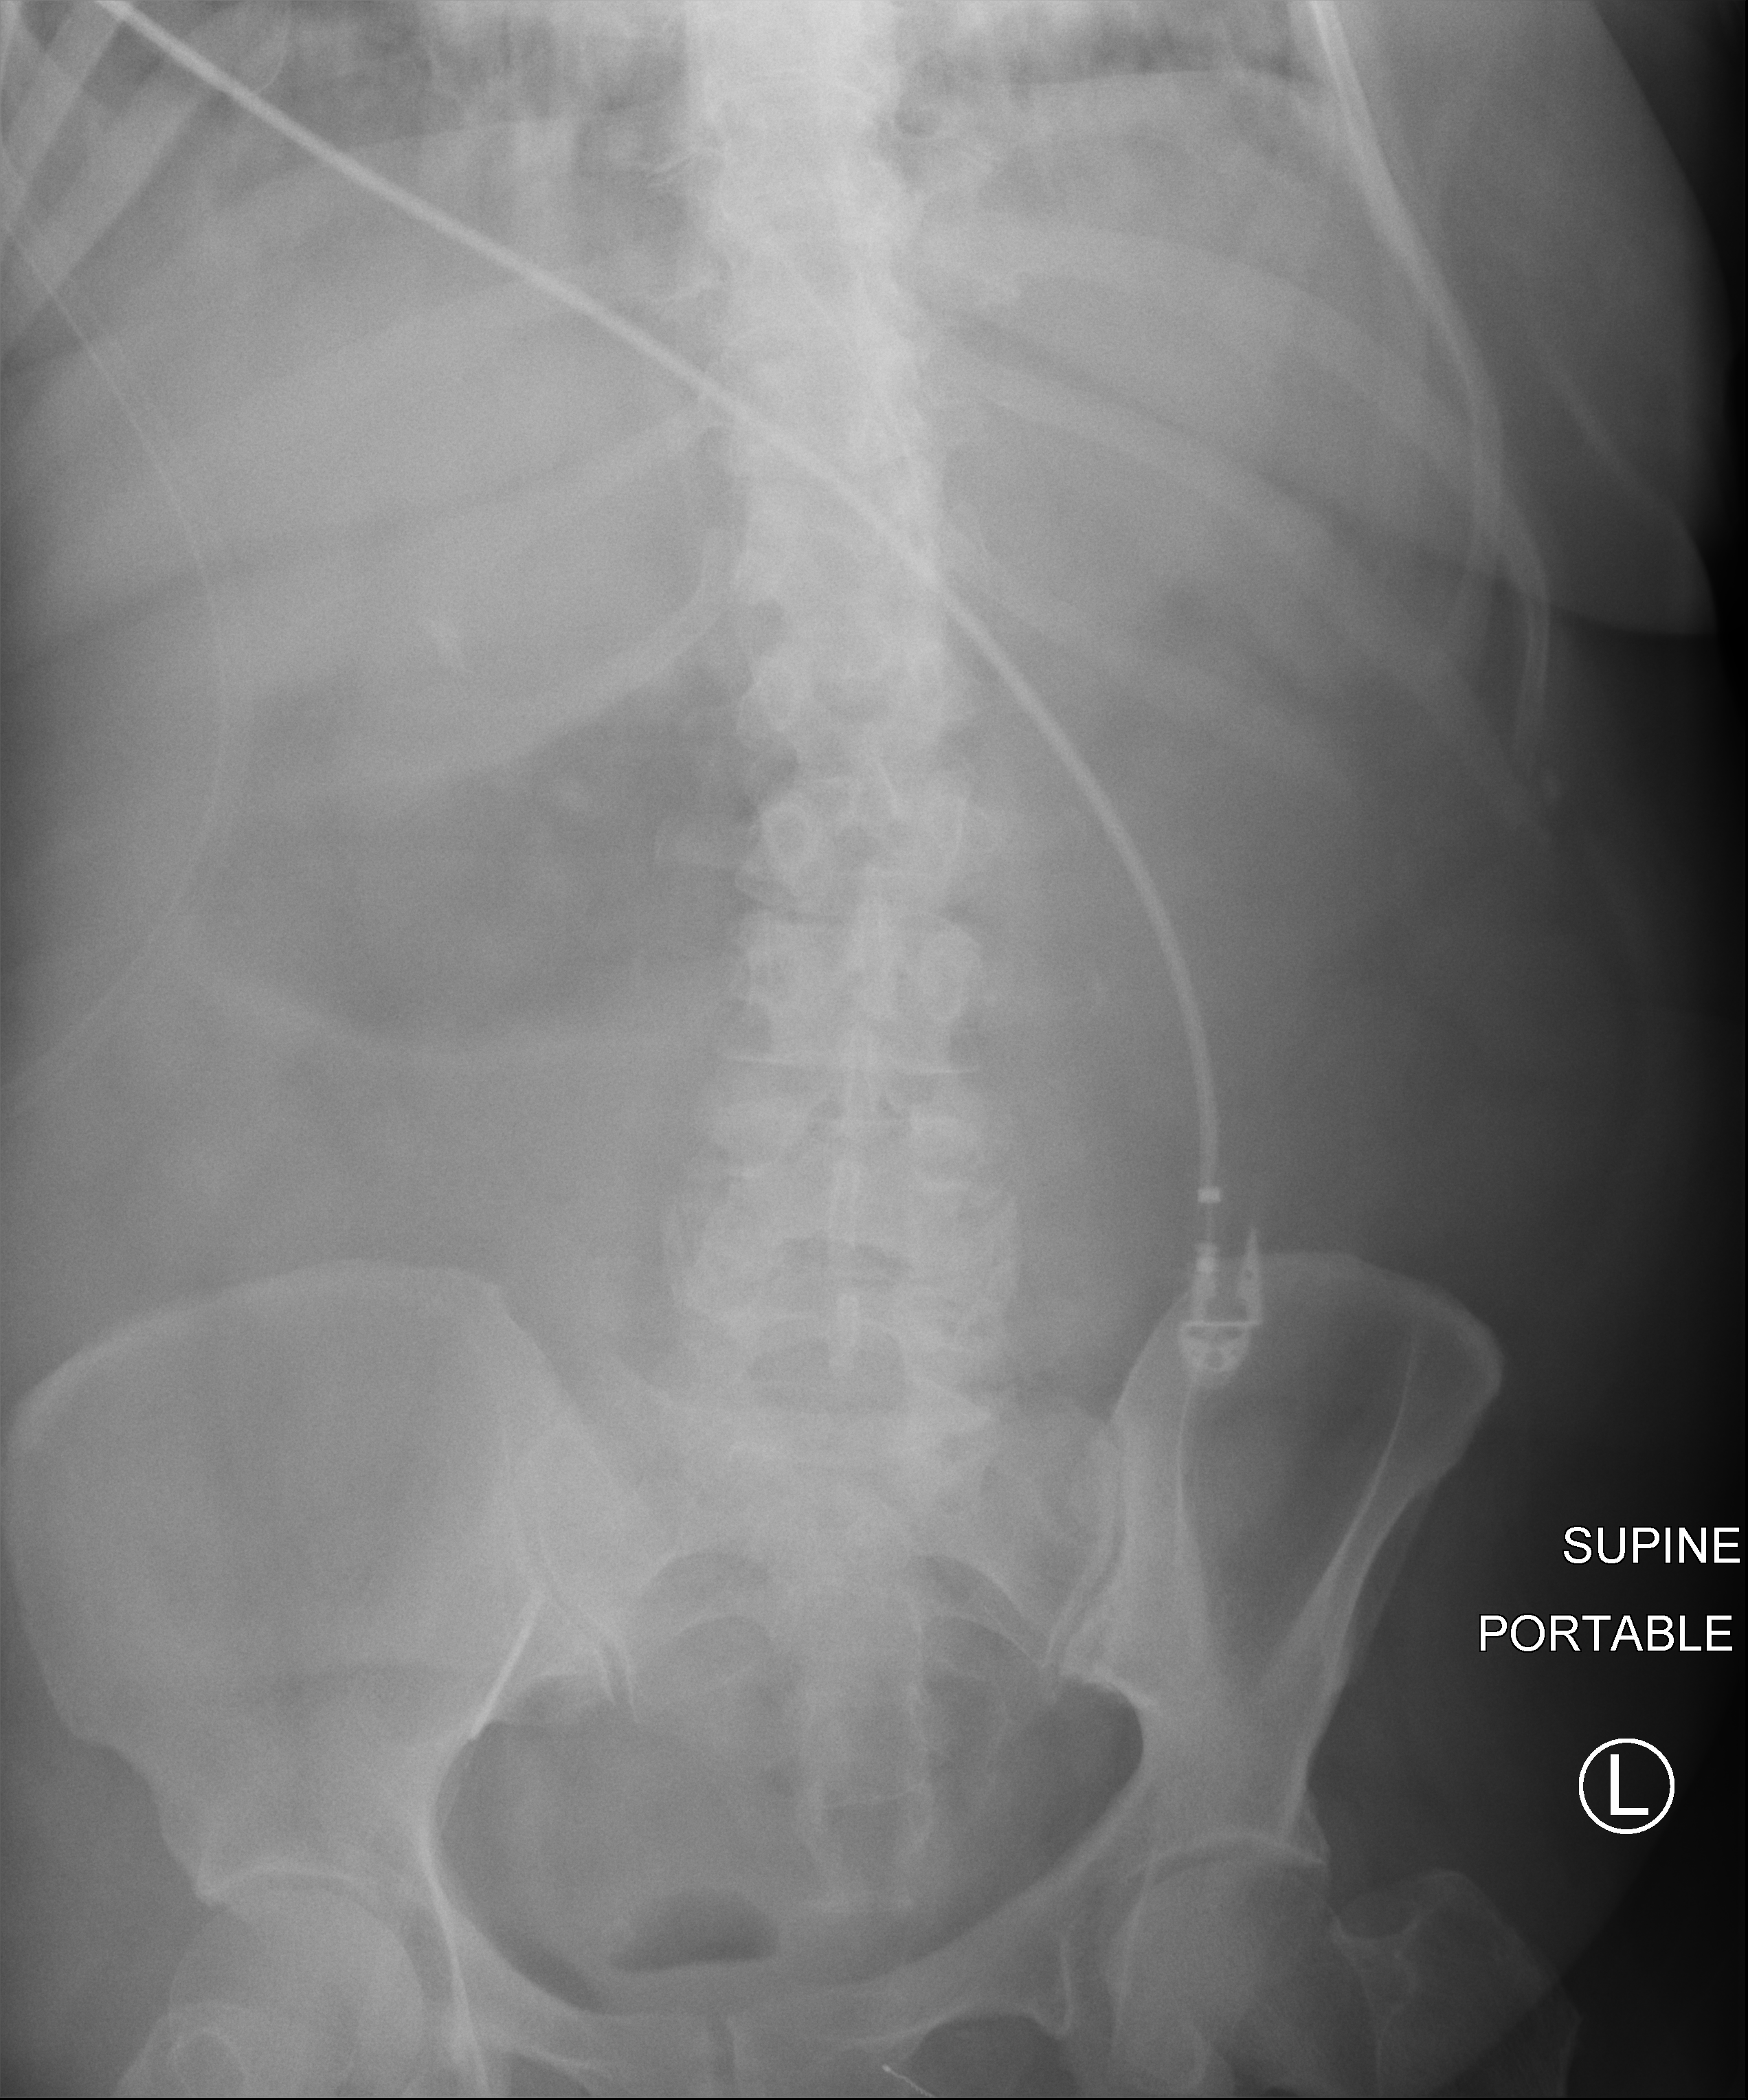
Bedside abdomen radiograph (computed radiography); anteroposterior (AP) projection. Patient hospitalised with COVID-19; female, aged 60–74 years.
Hospital-stay facts (about this admission, not read from this image; timing relative to this image not recorded): other chronic lung disease (admission record): yes; mechanically ventilated during this hospital stay: yes.